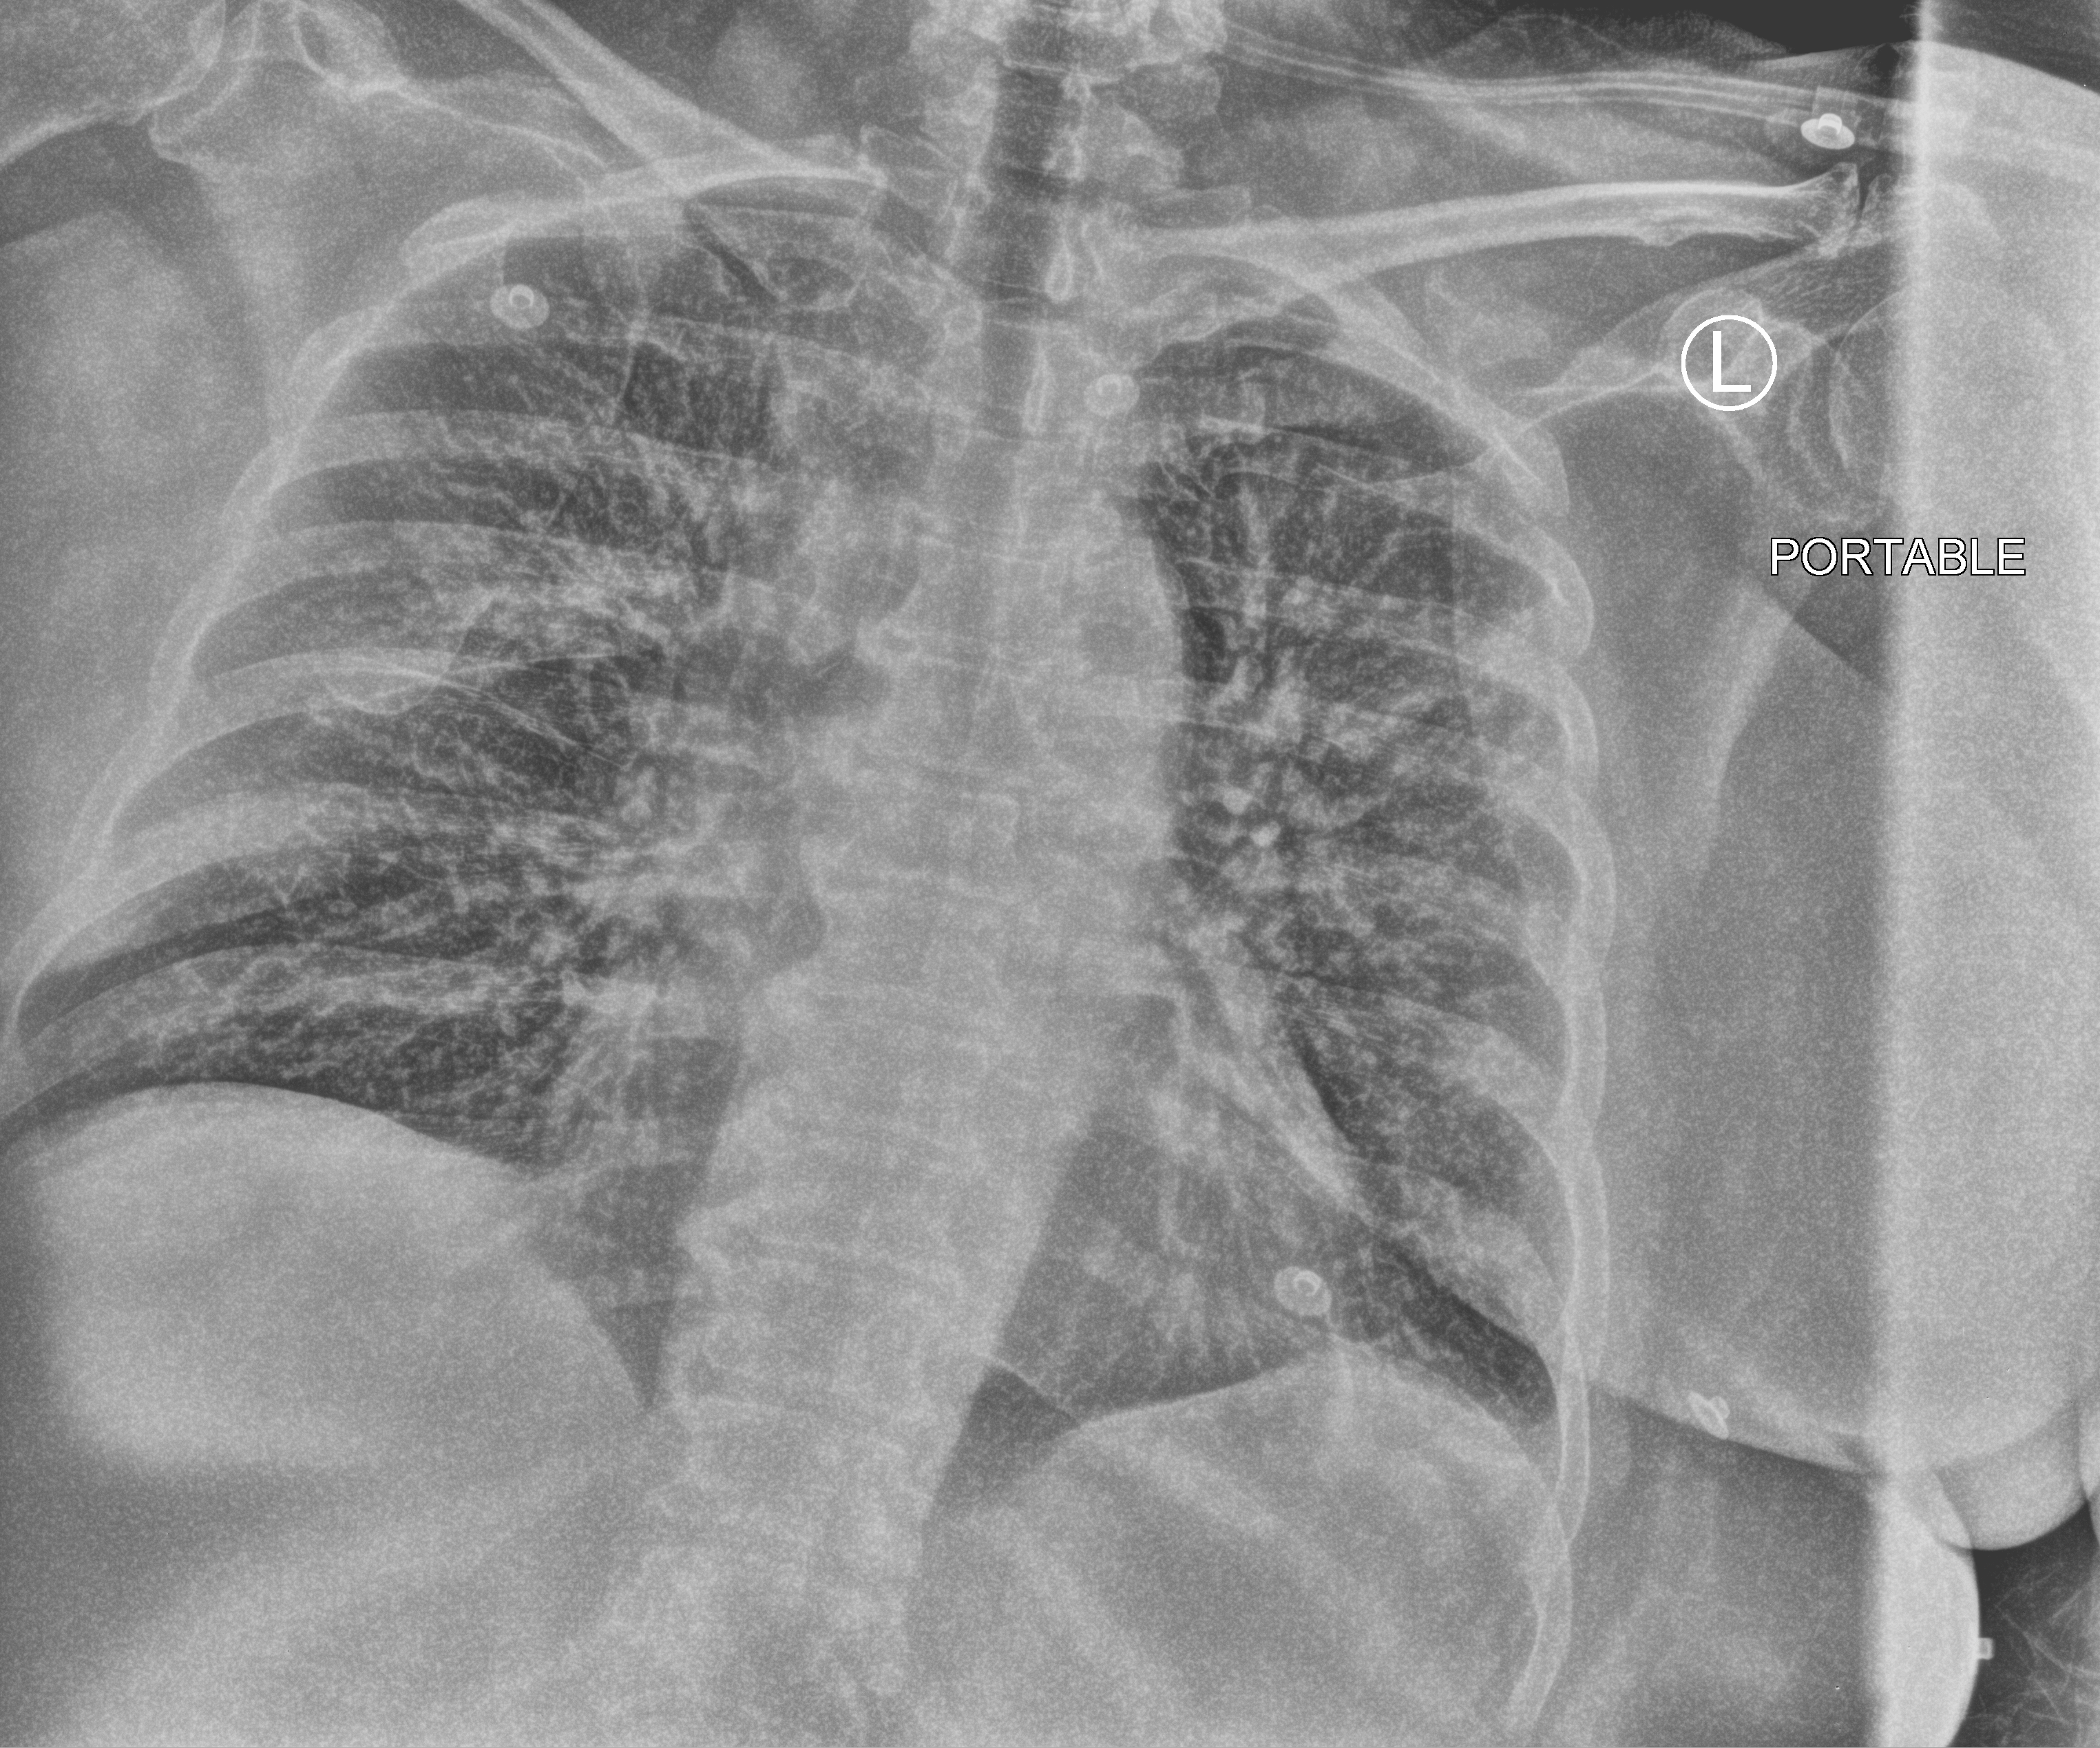
Portable chest radiograph, anteroposterior (AP) projection. Patient hospitalised with COVID-19; female, aged 60–74 years.
Admission-level facts for this patient (not findings on this image; timing relative to this image not recorded):
- mechanically ventilated during this hospital stay: no
- other chronic lung disease (admission record): no